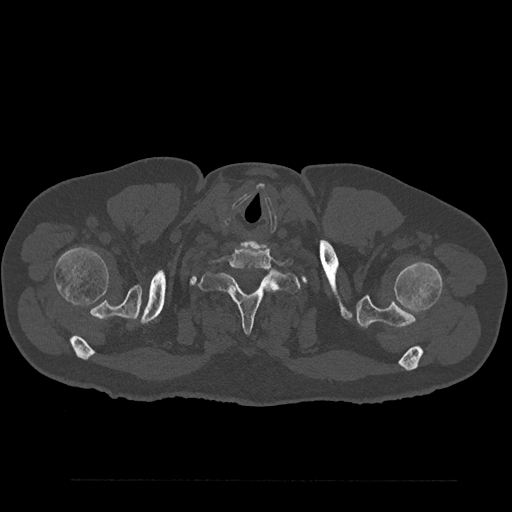
CT including the spine, one axial slice; position 761 of 797 along the scan axis; 120 kVp; bone window (W 1800 / L 400 HU); 0.5 mm slice thickness; 512 × 512 image matrix. Patient: male, 61 years. Case-level facts recorded for this patient, not image findings: primary cancer: prostate.
Annotated regions visible in this slice (semi-automatic segmentation, software-assisted and operator-edited):
- T1 vertebra: bounding box (x1, y1, x2, y2) in pixels: (199, 261, 301, 334)